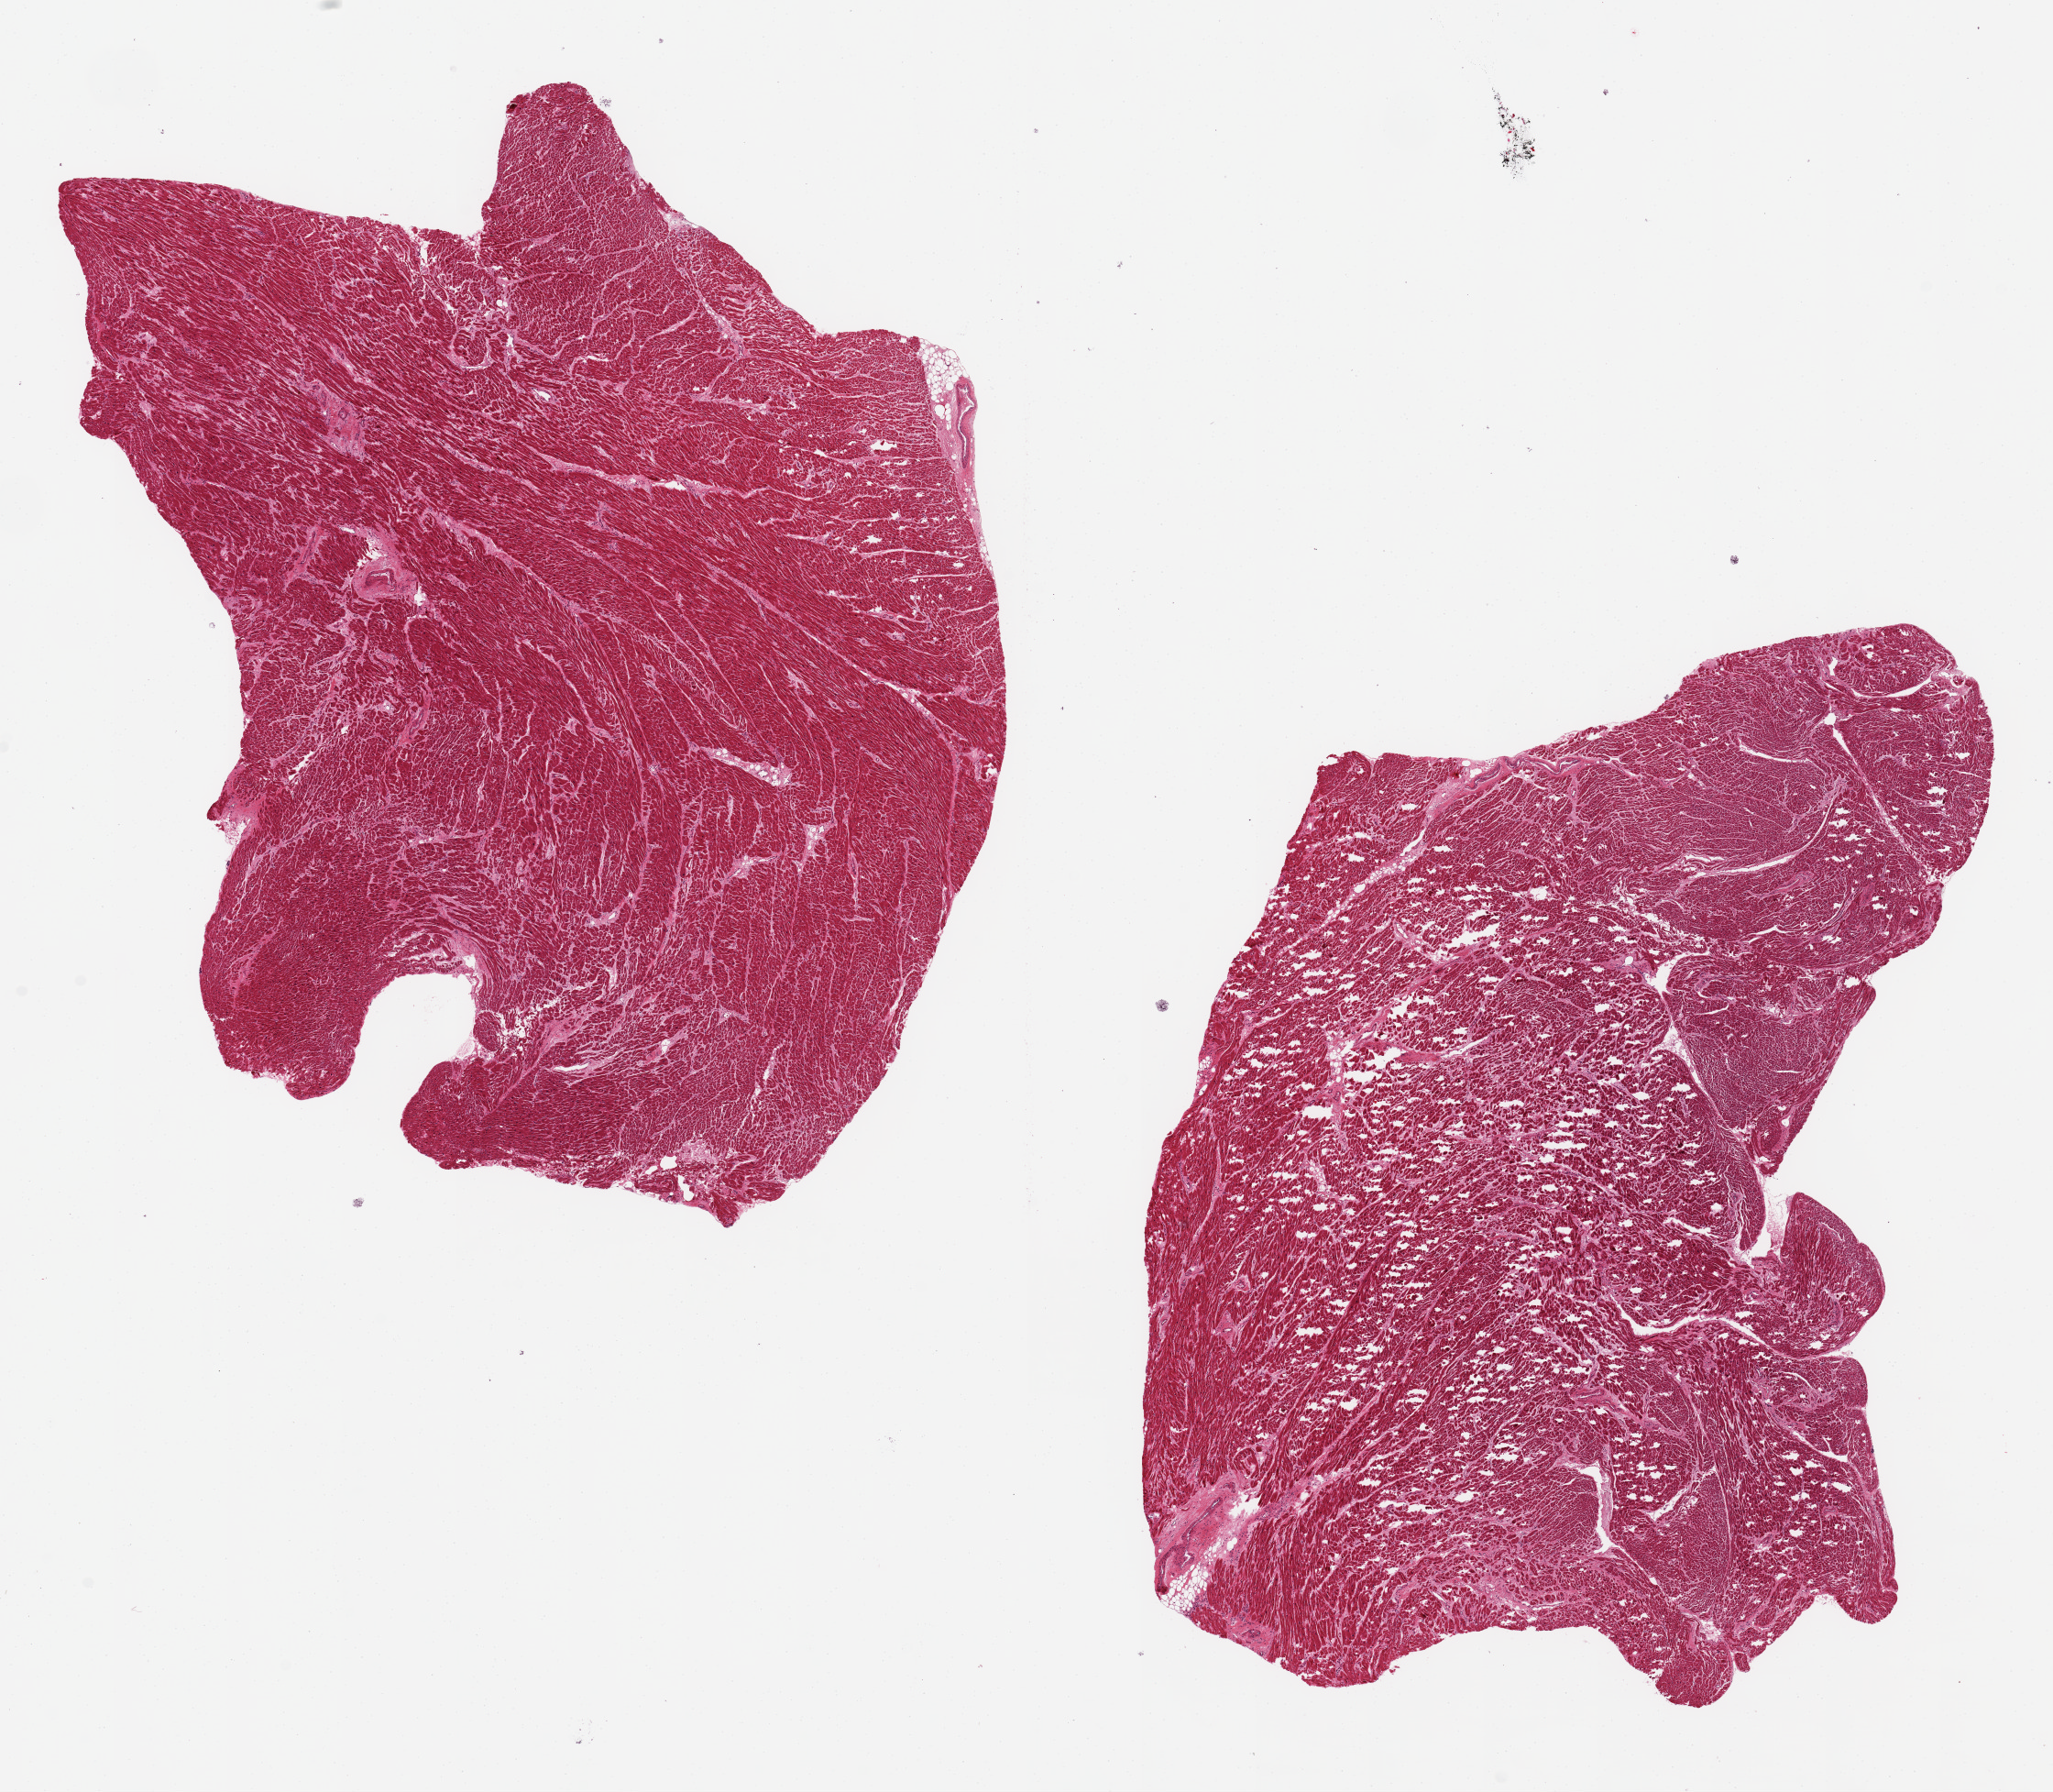
Whole-slide image, H&E stain, shown as a low-resolution overview of the whole scanned area (about 17.7 x 15.5 mm), PAXgene-fixed paraffin-embedded (PFPE) section, section of heart (target tissue), tissue donor sample. Male donor.
Reviewer comment on this tissue sample: 2 9x8mm aliquots, patchy interstitial fibrosis.